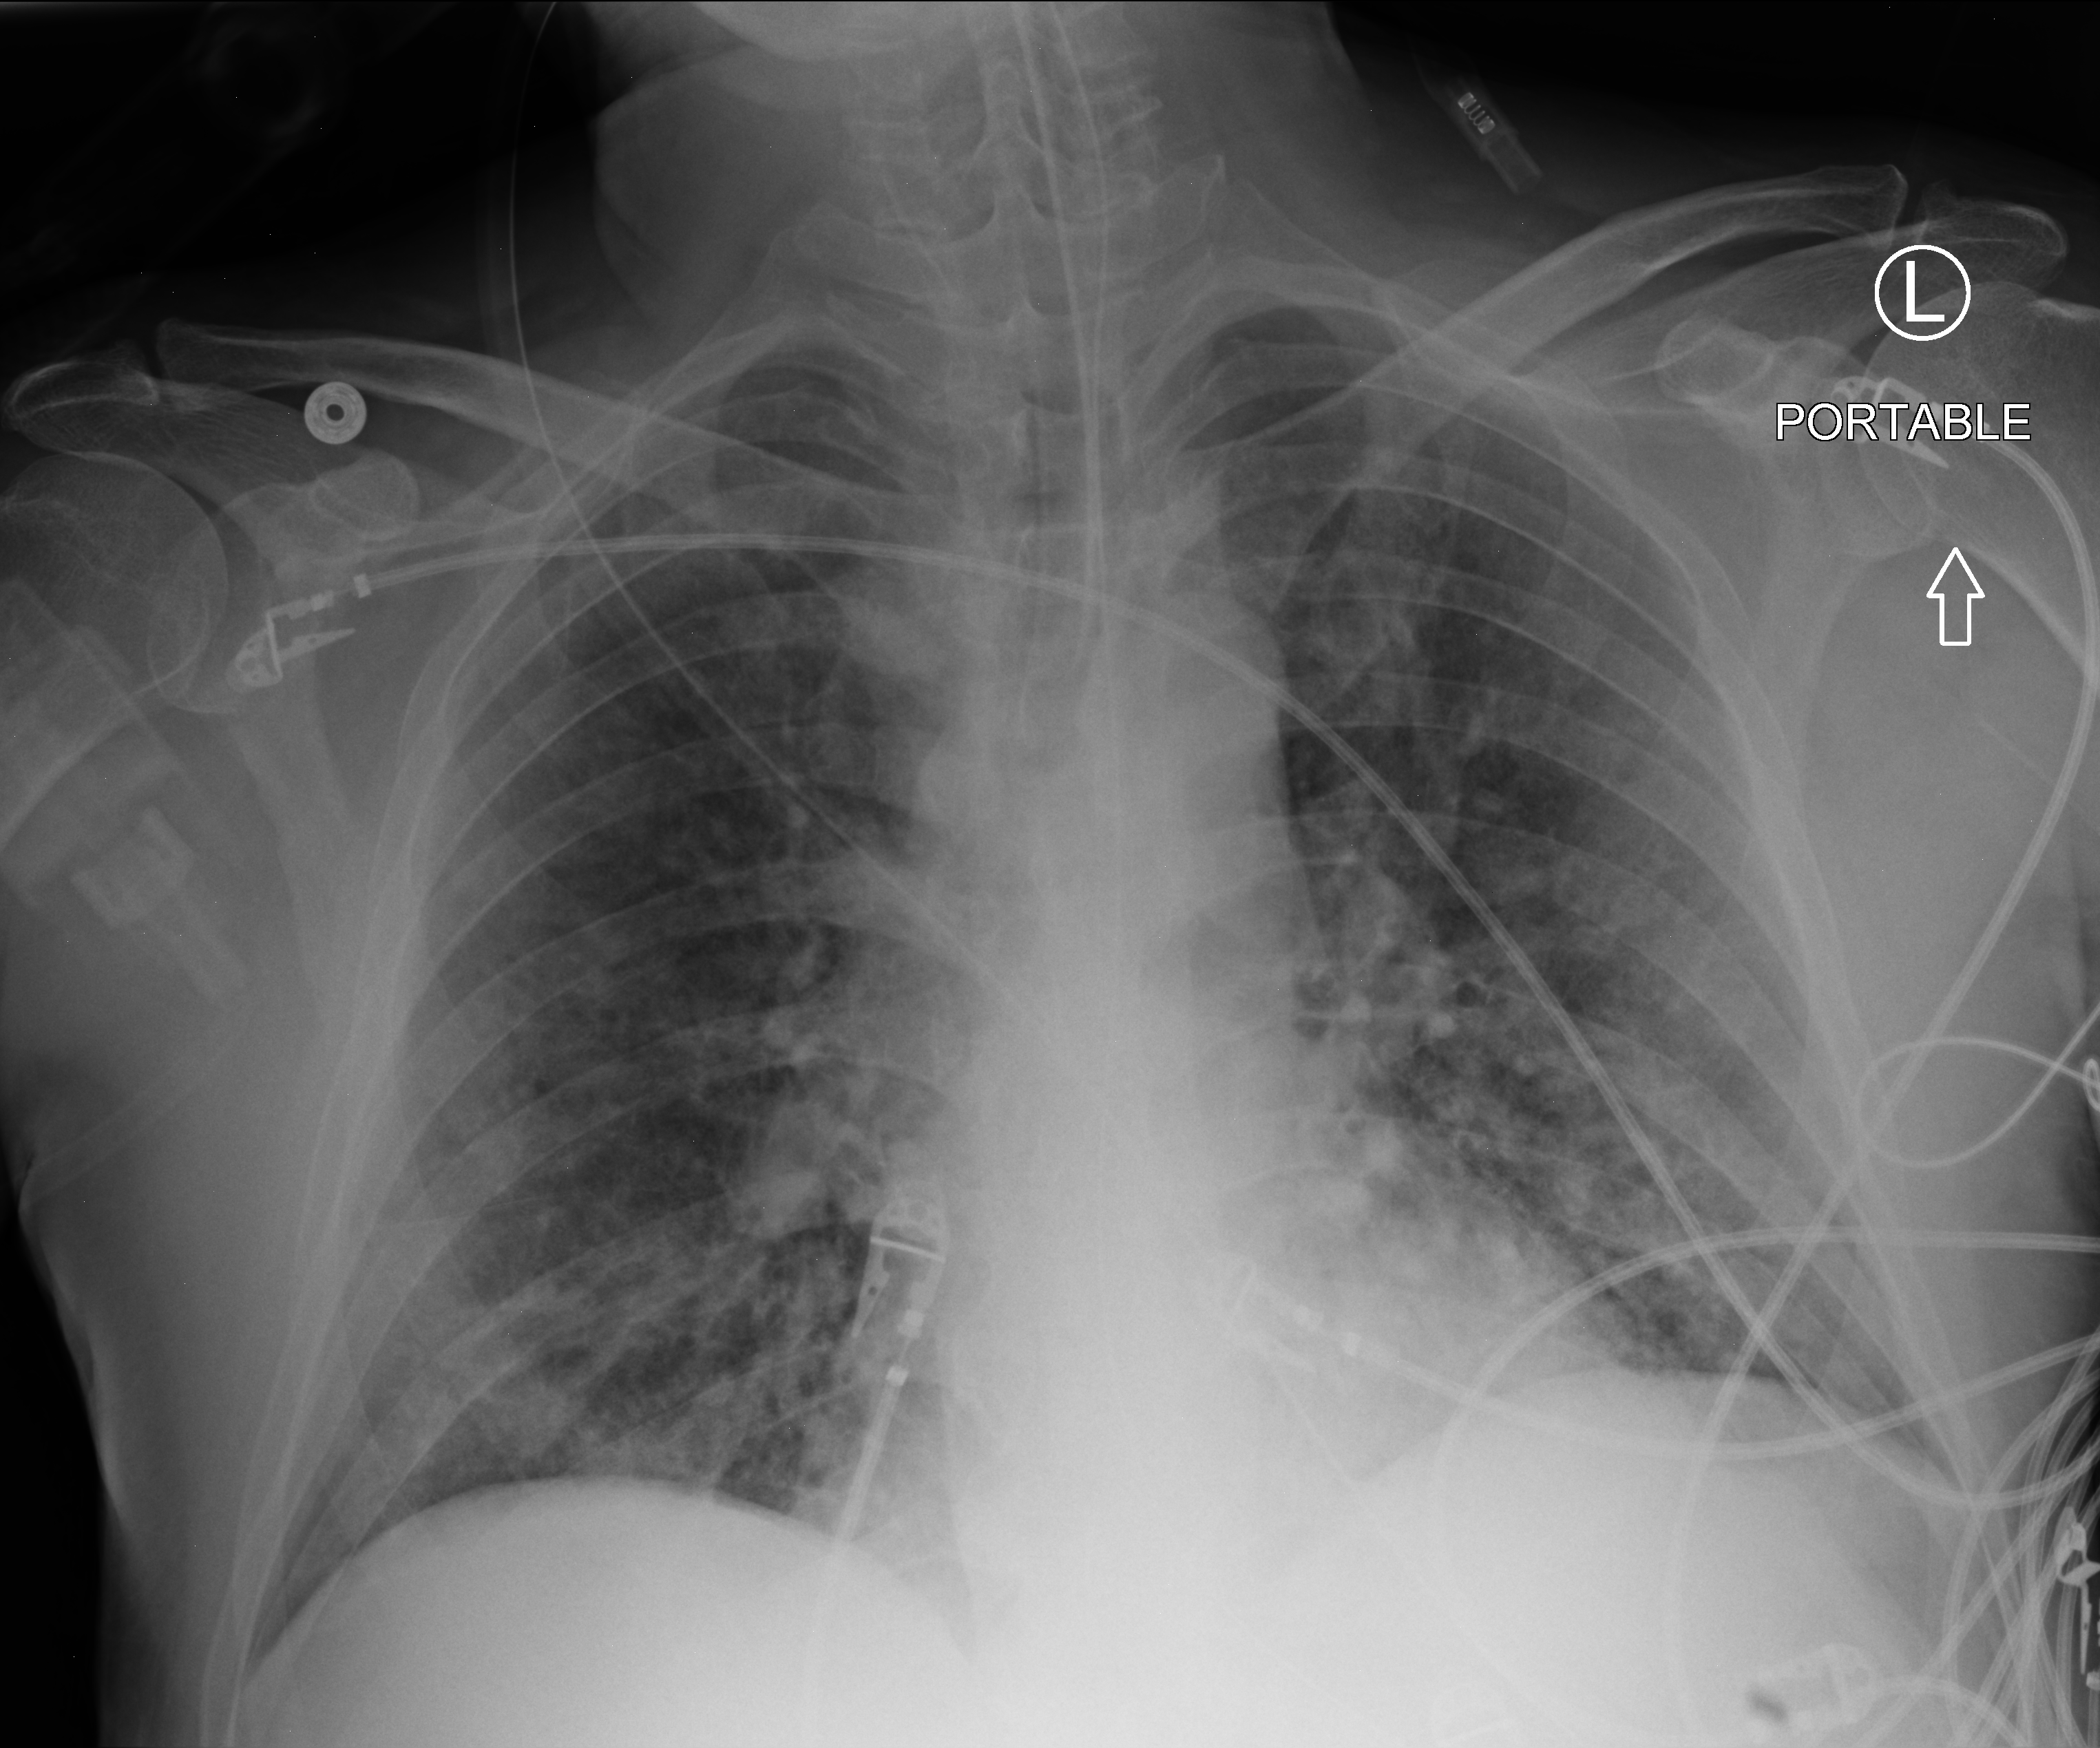
Bedside chest radiograph (computed radiography). Patient hospitalised with COVID-19; male, aged 18–59 years.
From the hospital-stay record, not from the radiograph (when in the stay this image was taken is not recorded): chronic kidney disease (admission record): no; mechanically ventilated during this hospital stay: yes.